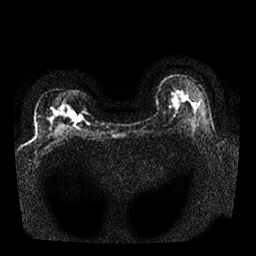
Breast MRI, one axial slice. Position 15 of 25 along the scan axis. Diffusion-weighted series; image 2 of 4 stored at this slice position (different b-values; order by instance number). 1.5 T. 4 mm slice thickness. 256 × 256 image matrix, field of view 340 × 340 mm. Female patient.
Annotated regions visible in this slice (manually delineated by an expert):
- tumour on diffusion-weighted imaging: bounding box <70,112,82,124> (left, top, right, bottom; pixels)